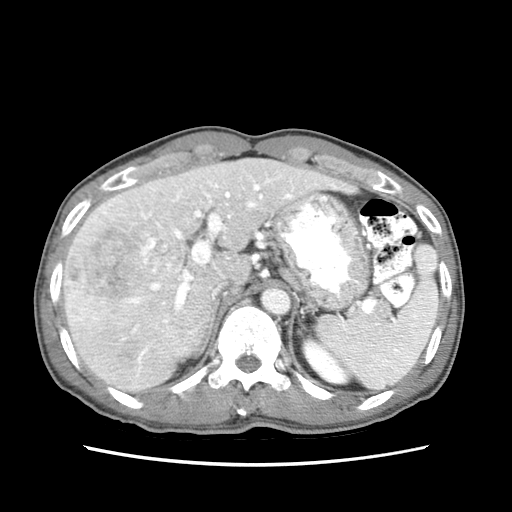
Contrast-enhanced abdominal CT (liver protocol), one axial slice; position 48 of 79 along the scan axis; reconstruction kernel STANDARD; soft-tissue window (W 400 / L 40 HU); 2.5 mm slice thickness; 512 × 512 image matrix, field of view 320 × 320 mm. Case-level facts recorded for this patient, not image findings: diagnosis: hepatocellular carcinoma (patient treated with transarterial chemoembolisation; whether this scan precedes or follows treatment is not stated here); TNM stage (as recorded): Stage-IIIB; Child-Pugh class: A; tumour differentiation: moderately differentiated.
Outlined on this slice (semi-automatic segmentation, software-assisted and operator-edited):
- liver parenchyma outside the tumour (the mass and vessels are separate outlines, so this box may not span the whole liver): box from (x=64, y=158) to (x=342, y=392) px
- mass: (x=62, y=203)–(x=141, y=328)
- liver vessels: (x=70, y=171)–(x=338, y=363)